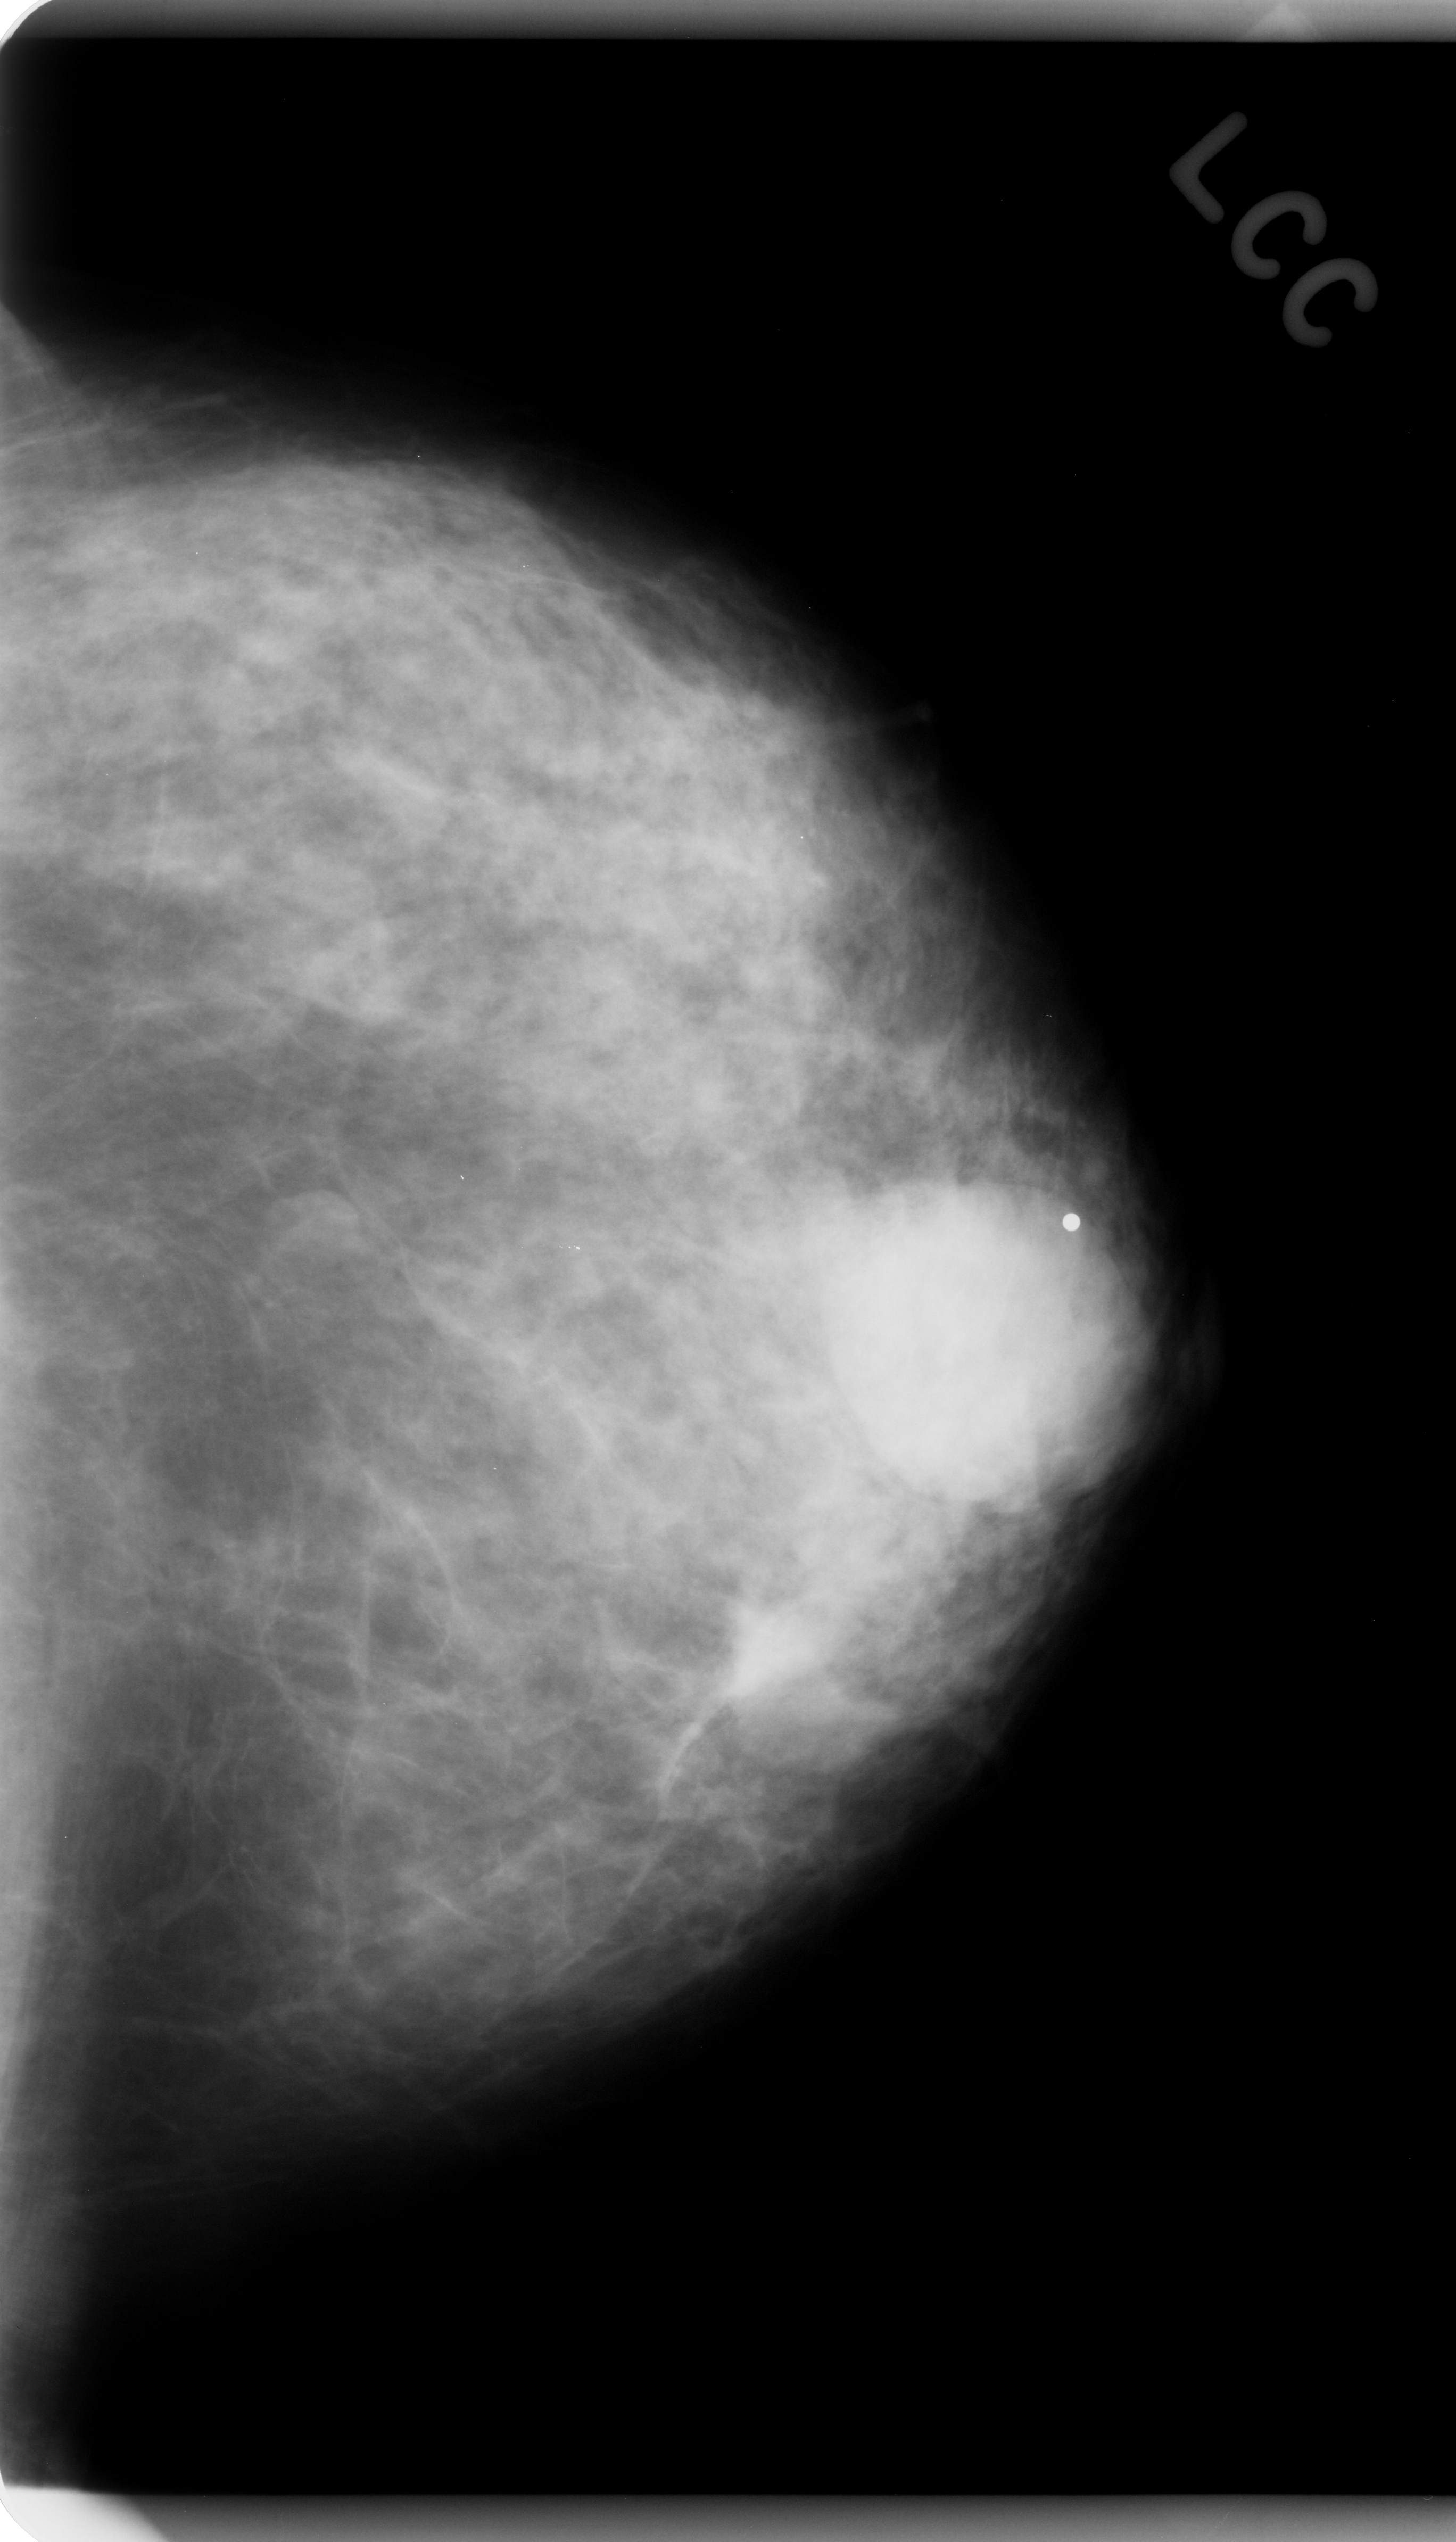
Digitized screen-film mammogram, left breast, craniocaudal (CC) view, breast composition: scattered fibroglandular densities (BI-RADS density category 2 of 4).
Abnormality record for this image: mass, shape round, margins obscured; BI-RADS assessment category 4; pathology (as recorded): benign.